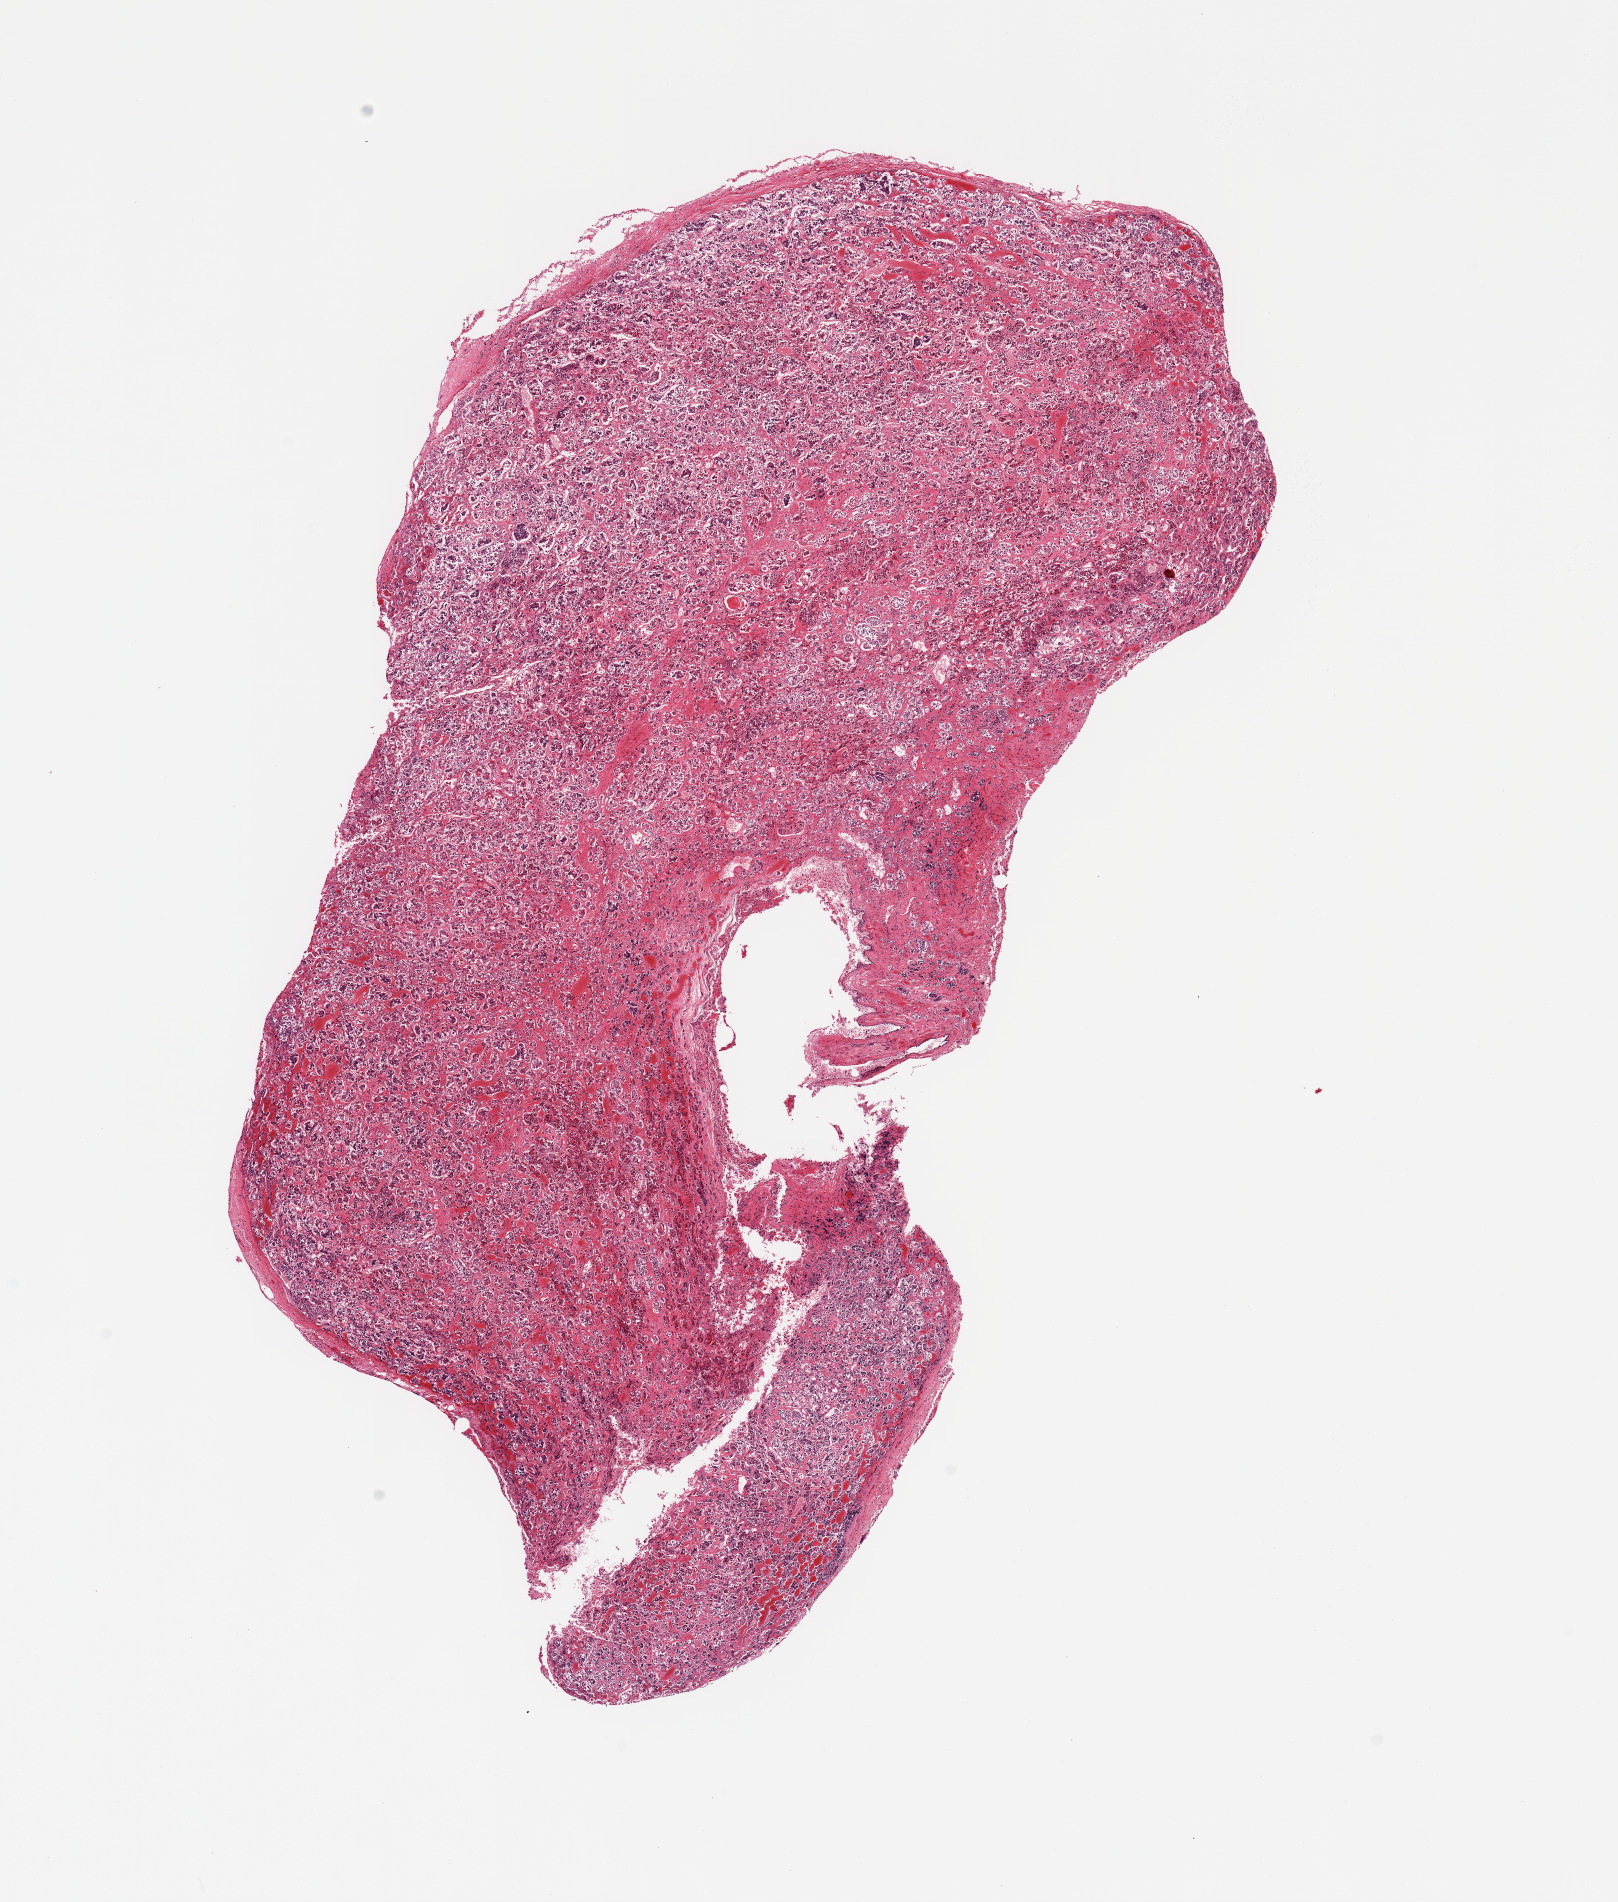
Haematoxylin and eosin whole-slide image, brightfield, low-resolution overview of the scanned area, about 12.8 x 15.0 mm, PAXgene-fixed paraffin-embedded (PFPE) section, target tissue: pituitary, tissue donor sample. Male donor.
Pathologist's review note for this sample: 1 piece; no neural component.